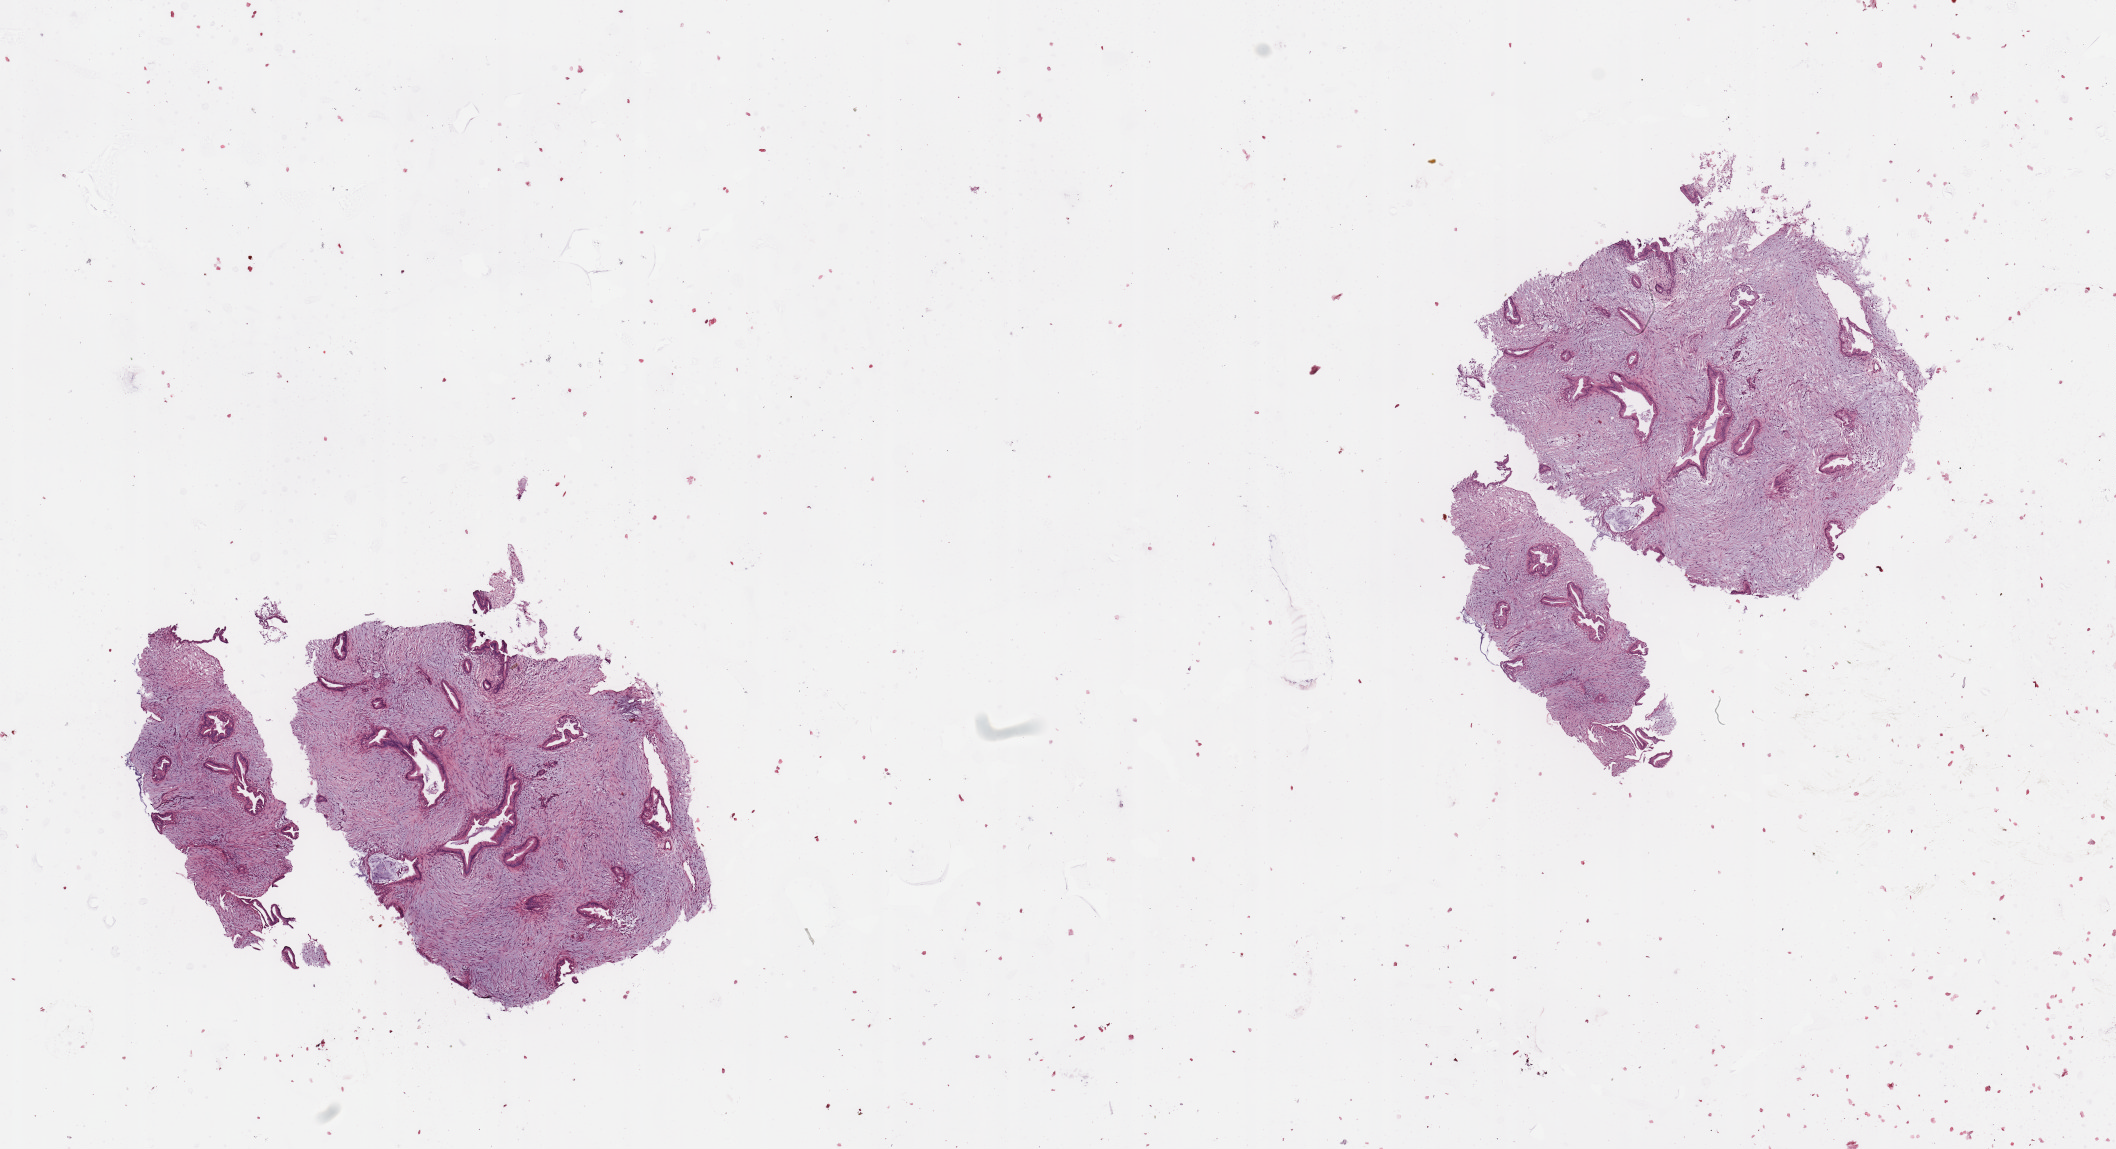
Whole-slide histology image, H&E-stained, whole scanned area (about 16.7 x 9.1 mm) shown as a low-resolution overview, tumour tissue sample, sampled site: pancreas. Patient: female, age 80 years. Histologic grade: G2 (moderately differentiated). Composition of this section per pathologist review: tumour nuclei 40%, necrosis 1%.
Histologic diagnosis: Infiltrating duct carcinoma, NOS. Primary tumour site (as recorded): head. AJCC pathologic stage: III.